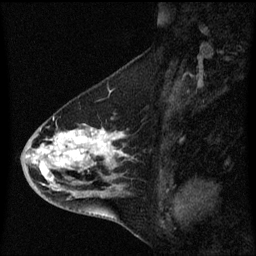
Breast MRI (dynamic contrast-enhanced), one sagittal slice; position 26 of 60 along the scan axis; dynamic contrast-enhanced series, image 2 of 3 at this slice position (ordered by acquisition); 1.5 T; TE 4.2 ms, TR 8.4 ms; 2 mm slice thickness; 256 × 256 image matrix, field of view 200 × 200 mm. Female patient, age 46 years. From the clinical record (not read from this slice): setting: breast cancer imaged before/during neoadjuvant chemotherapy; receptor status: HER2-positive.
Structures marked on this image (semi-automatically segmented with operator editing):
- analysis volume of interest (the breast-tissue region the enhancement analysis was run in; not a lesion): bounding box (x1, y1, x2, y2) in pixels: (21, 114, 132, 195)
- tumour enhancement mask (voxels above the 70 % enhancement threshold inside the analysis volume of interest): (35, 130, 127, 181)